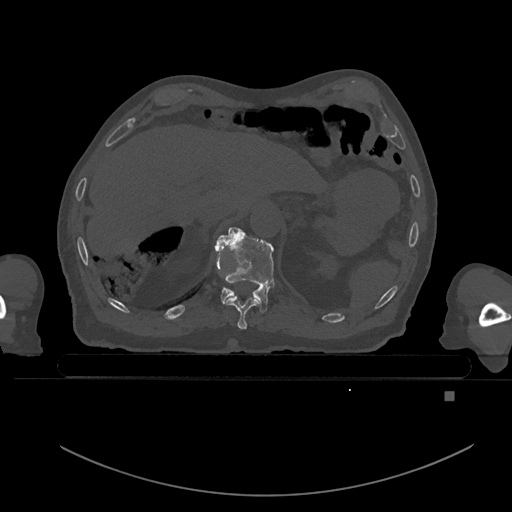
CT including the spine, one axial slice. Position 55 of 969 along the scan axis. Bone window (W 1800 / L 400 HU). 0.5 mm slice thickness. 512 × 512 image matrix. Male patient, age 82 years. Case-level facts recorded for this patient, not image findings: primary cancer: prostate; vertebrae with lytic lesions (as recorded): T11, T9, T8, T2.
Structures marked on this image (semi-automatically segmented with operator editing):
- T10 vertebra: box from (x=225, y=296) to (x=260, y=330) px
- T11 vertebra: (x=216, y=227)–(x=274, y=313)